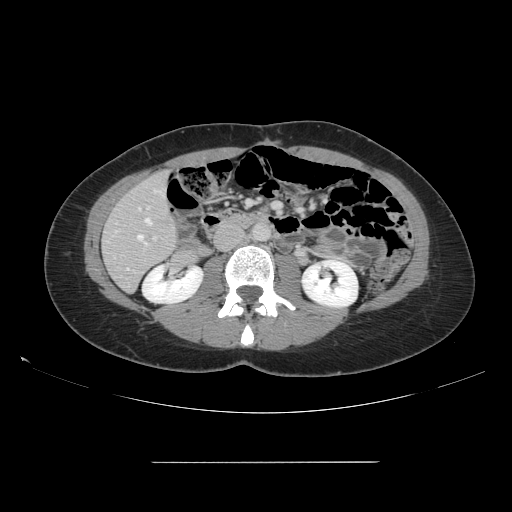
Contrast-enhanced abdominal CT, one axial slice. Position 52 of 151 along the scan axis. 120 kVp. Intravenous contrast given. Soft-tissue window (W 400 / L 40 HU). 2.5 mm slice thickness. 512 × 512 image matrix, field of view 421 × 421 mm. Female patient, age 46 years. Case-level facts recorded for this patient, not image findings: diagnosis: colorectal cancer liver metastases, imaged before liver resection; multiple liver metastases: yes; largest metastasis: 3 cm.
Outlined on this slice (expert manual segmentation):
- hepatic veins: bounding box [x1, y1, x2, y2] px = [138, 218, 152, 240]
- liver: [104, 173, 177, 291]
- planned liver remnant (the part of the liver to remain after resection): [104, 173, 177, 291]
- portal vein (with intrahepatic branches): [154, 237, 156, 240]